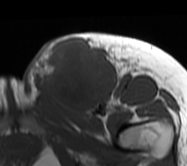
MRI of an extremity soft-tissue mass, one axial slice; position 29 of 62 along the scan axis; MR volume resampled by the dataset authors to the PET/CT grid (not the native acquisition matrix); 3.27 mm slice thickness; 187 × 166 image matrix, field of view 183 × 162 mm. Female patient. From the clinical record (not read from this slice): histological type: leiomyosarcoma; grade: high; site of the primary tumour: groin.
Outlined on this slice (expert contour drawn on MRI and transferred to this co-registered scan by the dataset authors):
- gross tumour volume including surrounding oedema: box from (x=25, y=31) to (x=136, y=118) px
- gross tumour volume (mass): (x=30, y=37)–(x=117, y=114)